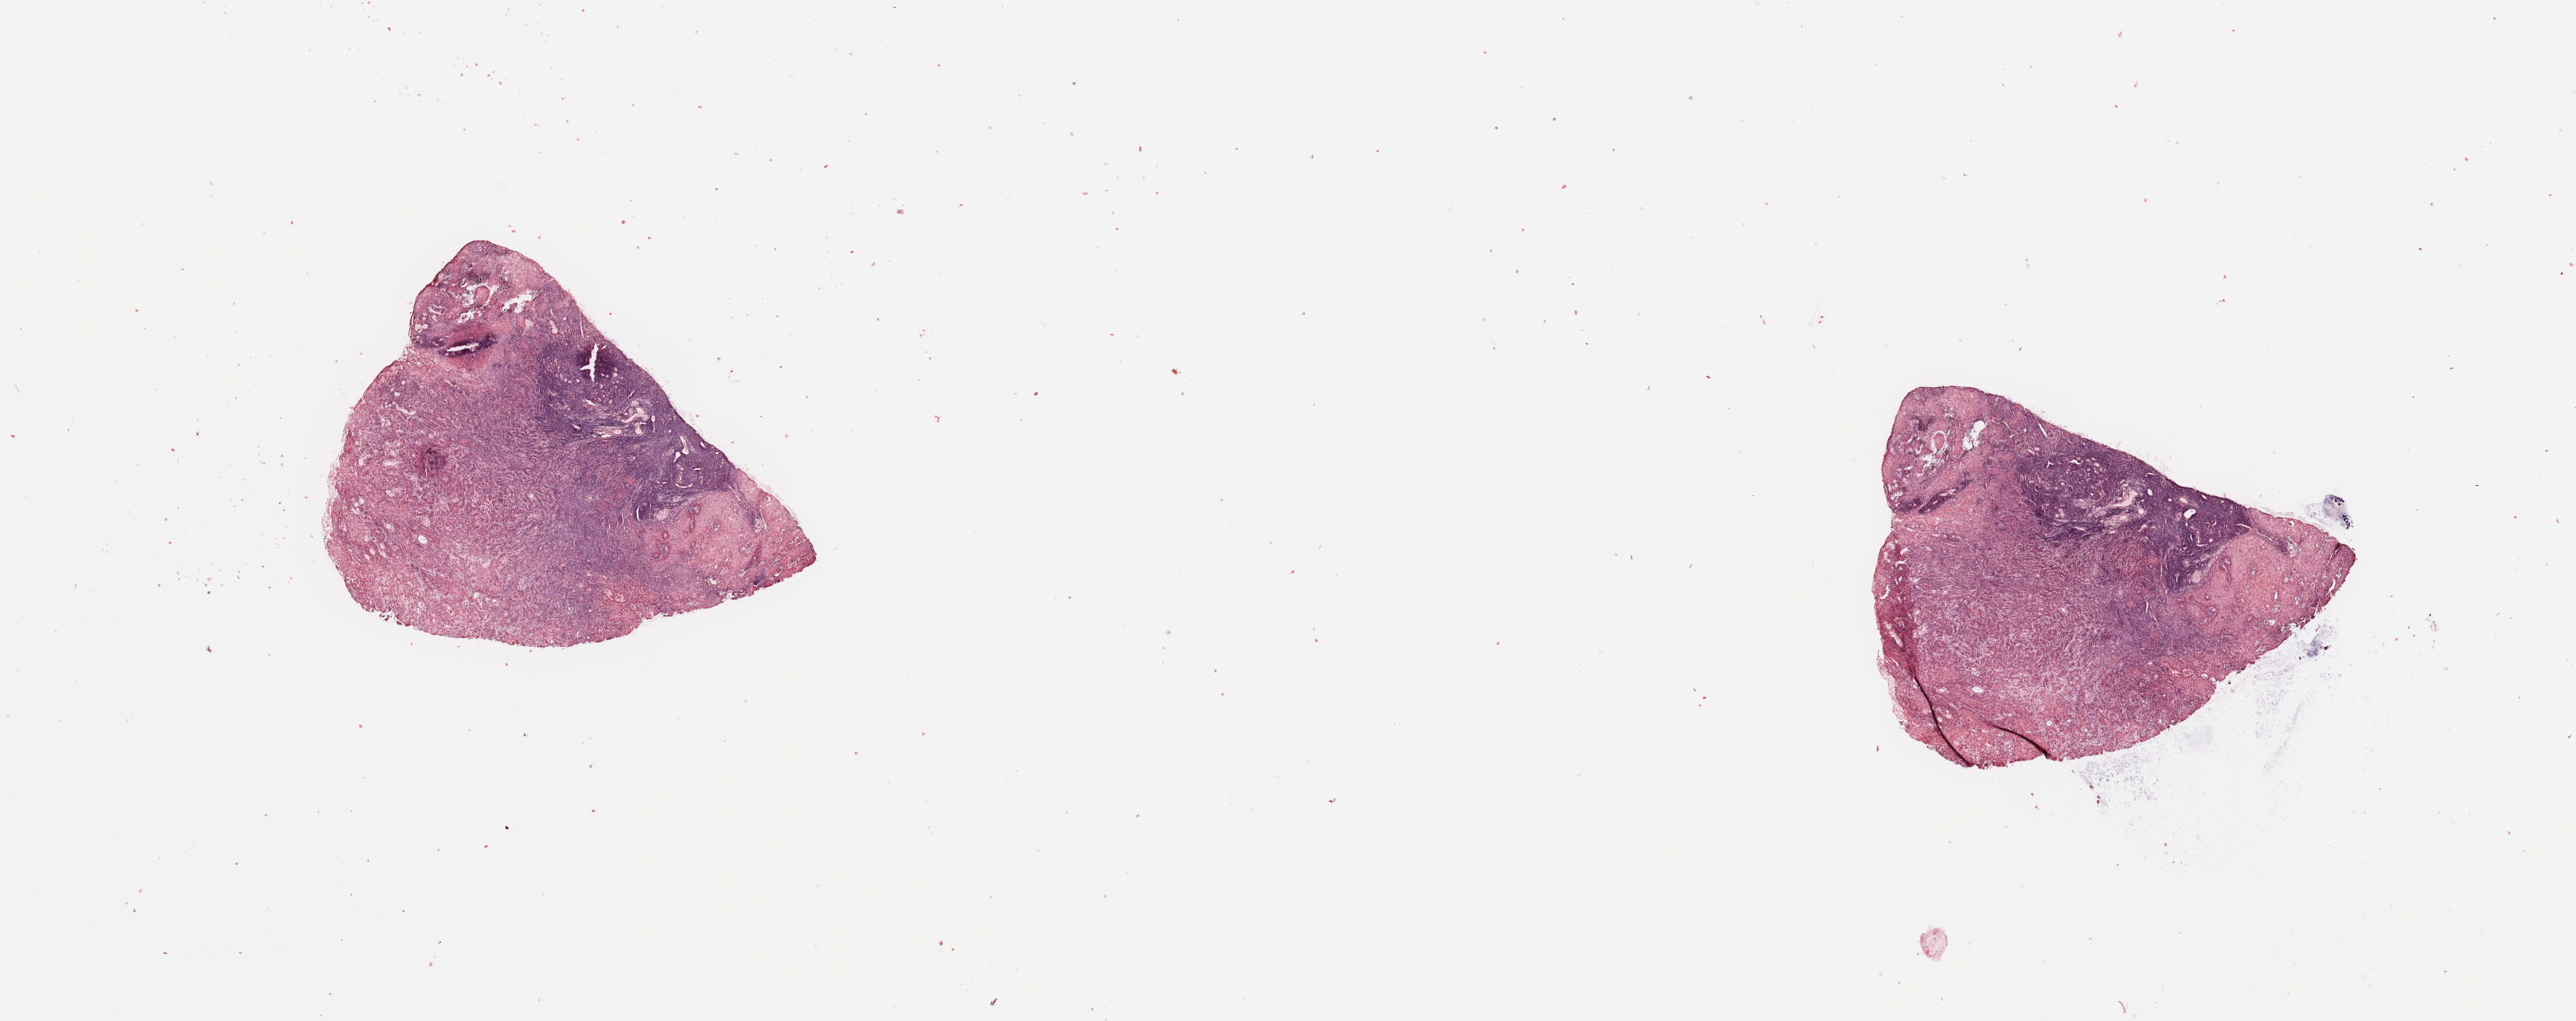
Hematoxylin and eosin (H&E) stained whole-slide image — a low-resolution overview of the entire scanned area, about 25.6 x 10.1 mm (from a 20x scan); head and neck, tissue type not recorded. 55-year-old female patient.
Patient diagnosis: Squamous cell carcinoma, NOS (tongue, NOS).